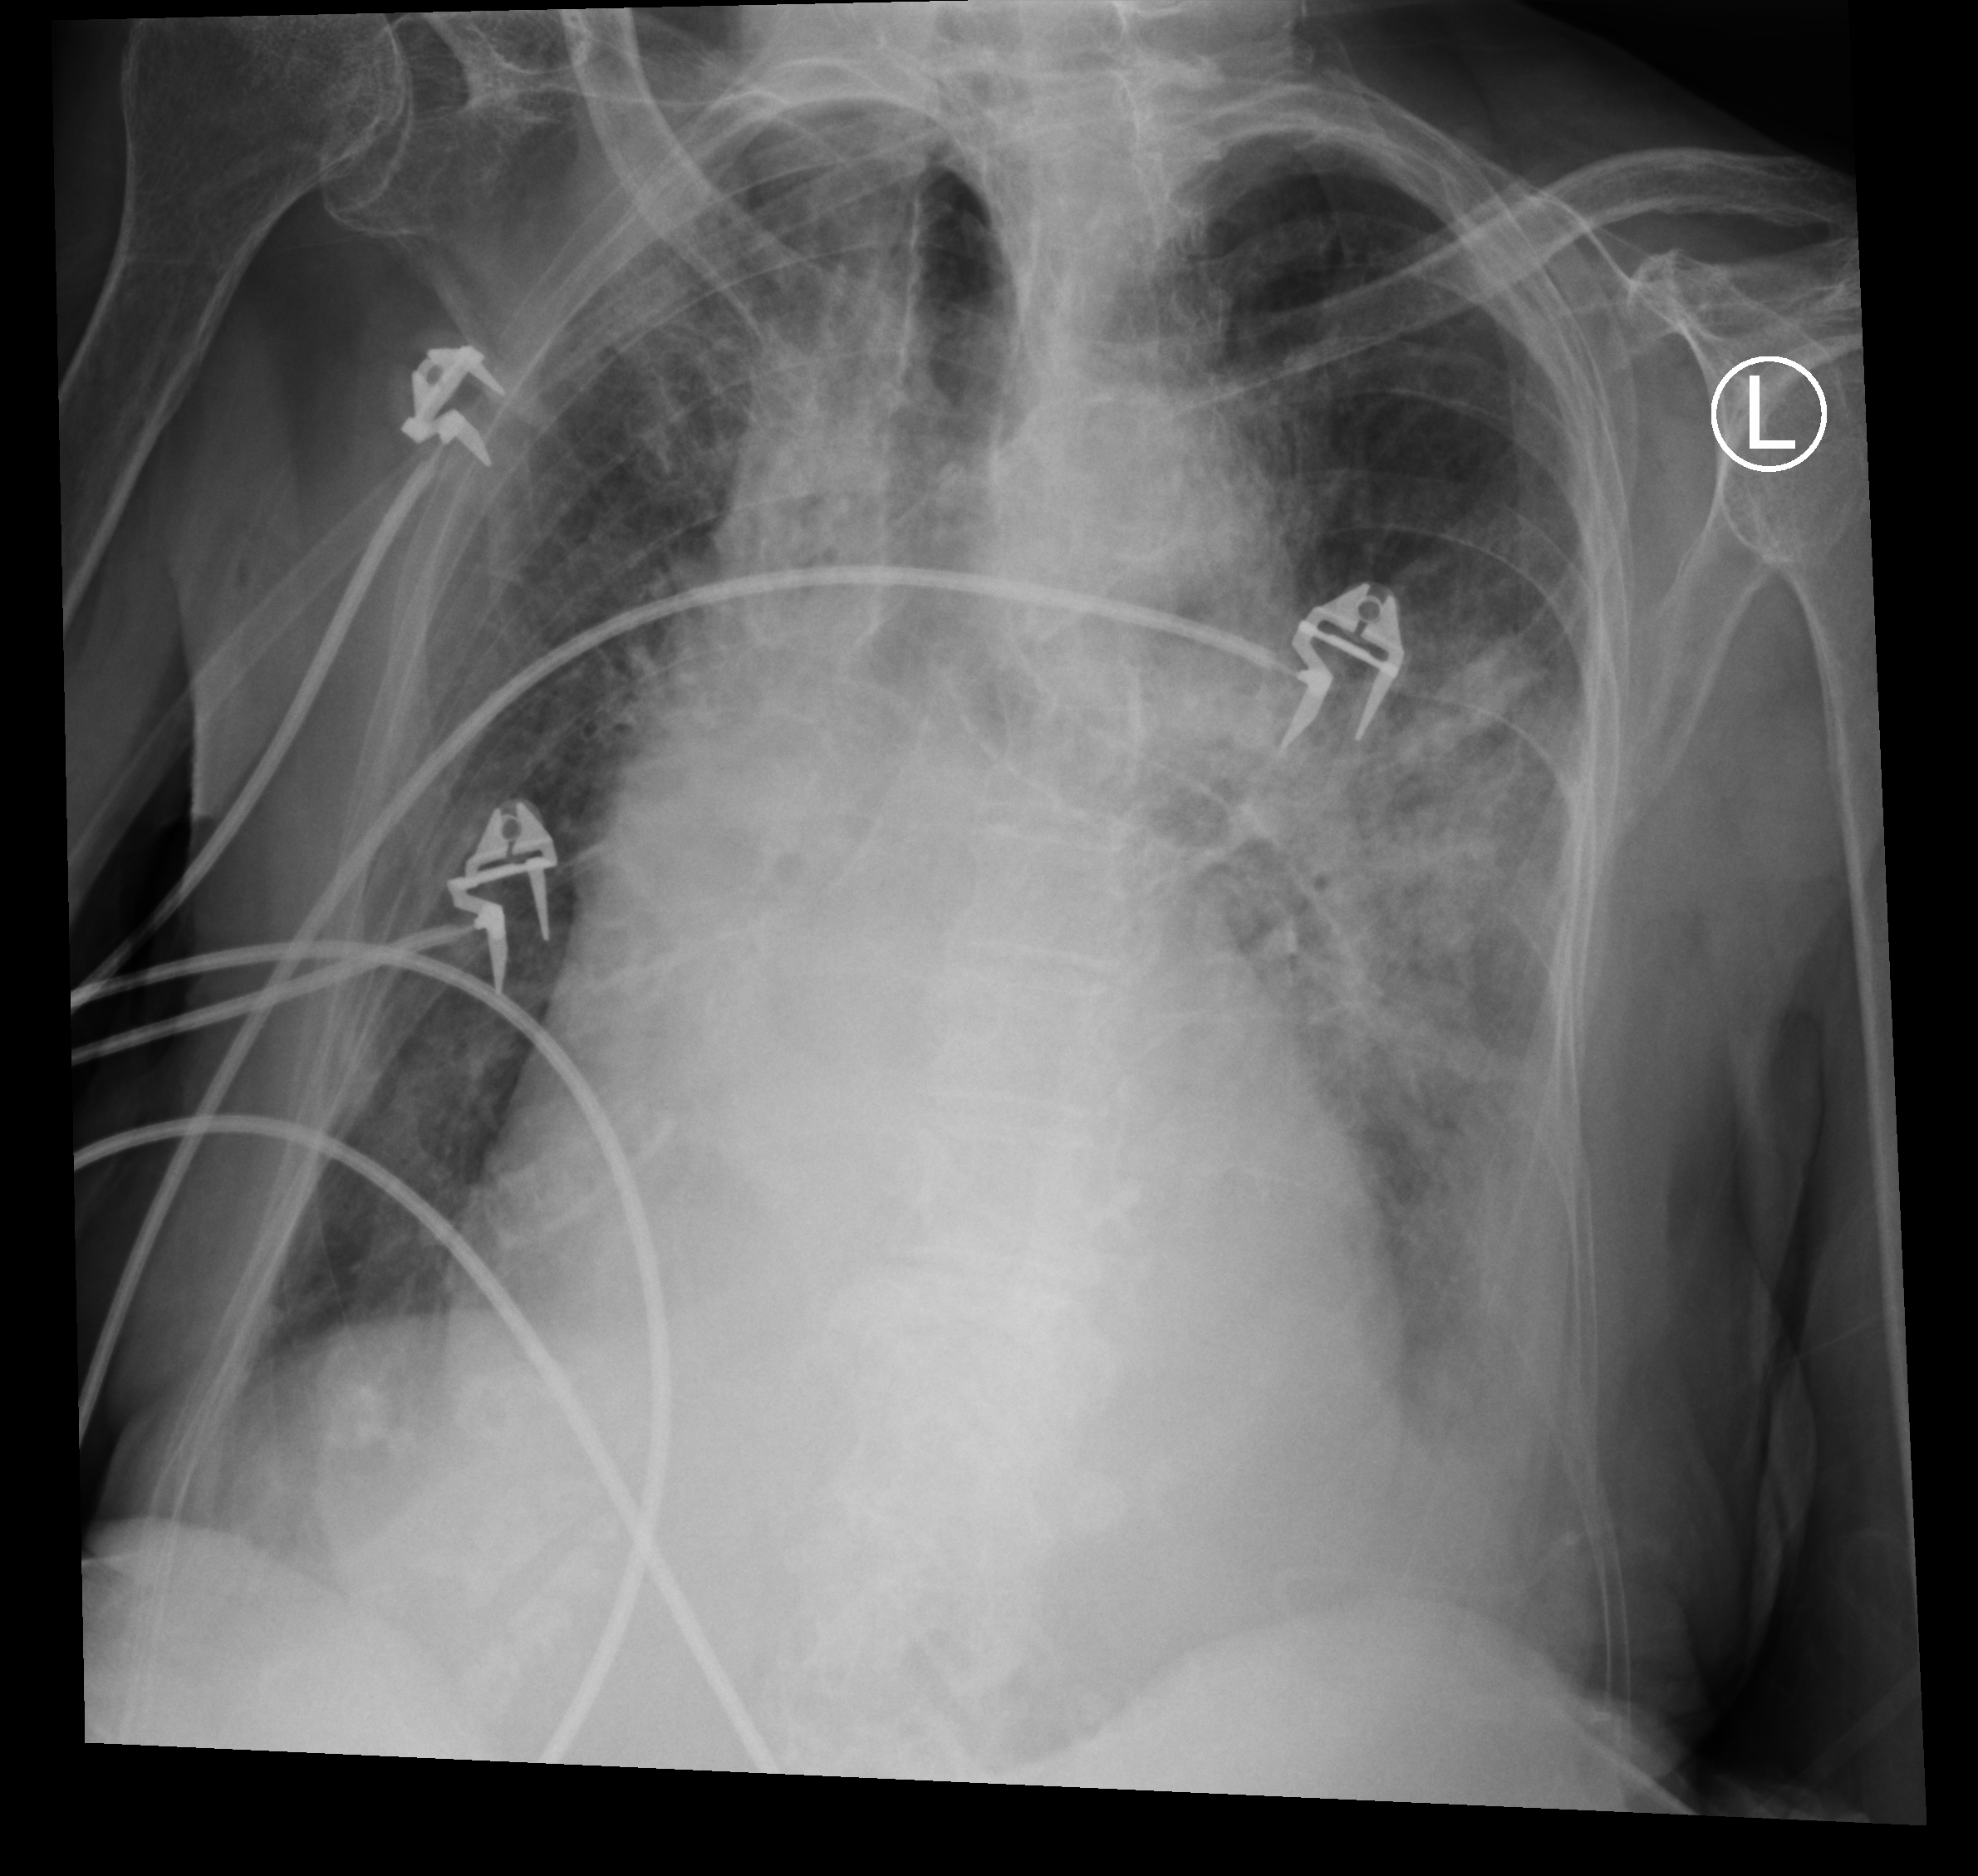
Bedside chest radiograph (computed radiography), anteroposterior (AP) projection. Patient hospitalised with COVID-19; female, aged 75–90 years.
From the hospital-stay record, not from the radiograph (when in the stay this image was taken is not recorded): mechanically ventilated during this hospital stay: no.